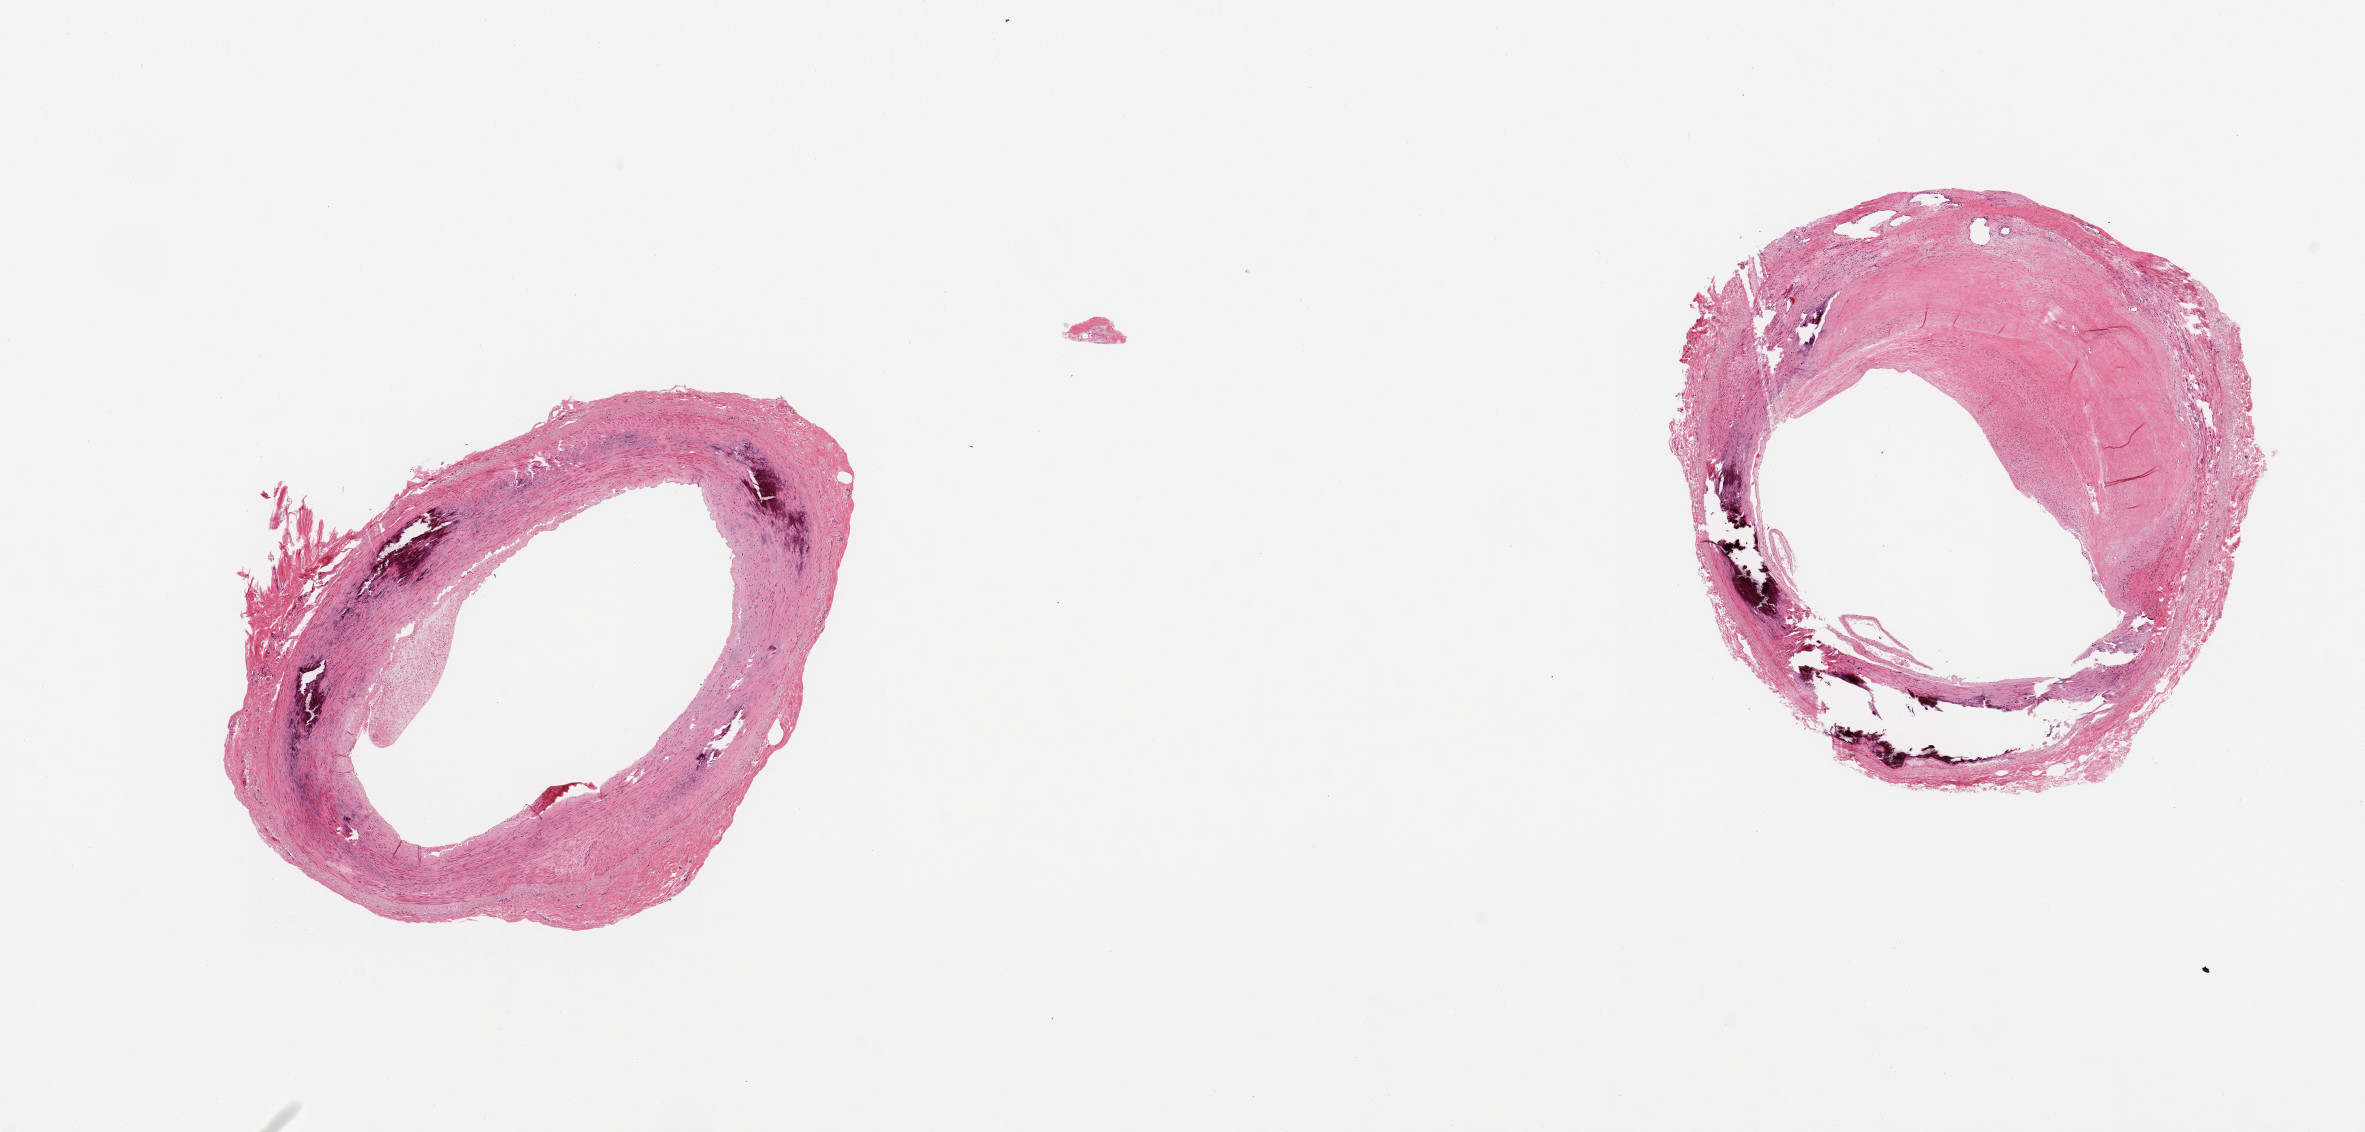
Digitized haematoxylin and eosin-stained section — shown as a low-resolution overview of the whole scanned area (about 18.7 x 9.0 mm, slide scanned at 20x), PAXgene-fixed paraffin-embedded (PFPE) section, section of tibial artery (target tissue), tissue donor sample. Donor sex: female.
Review note (as recorded): 2 pieces, ~70% occlusive focally aclicifying atherosis.